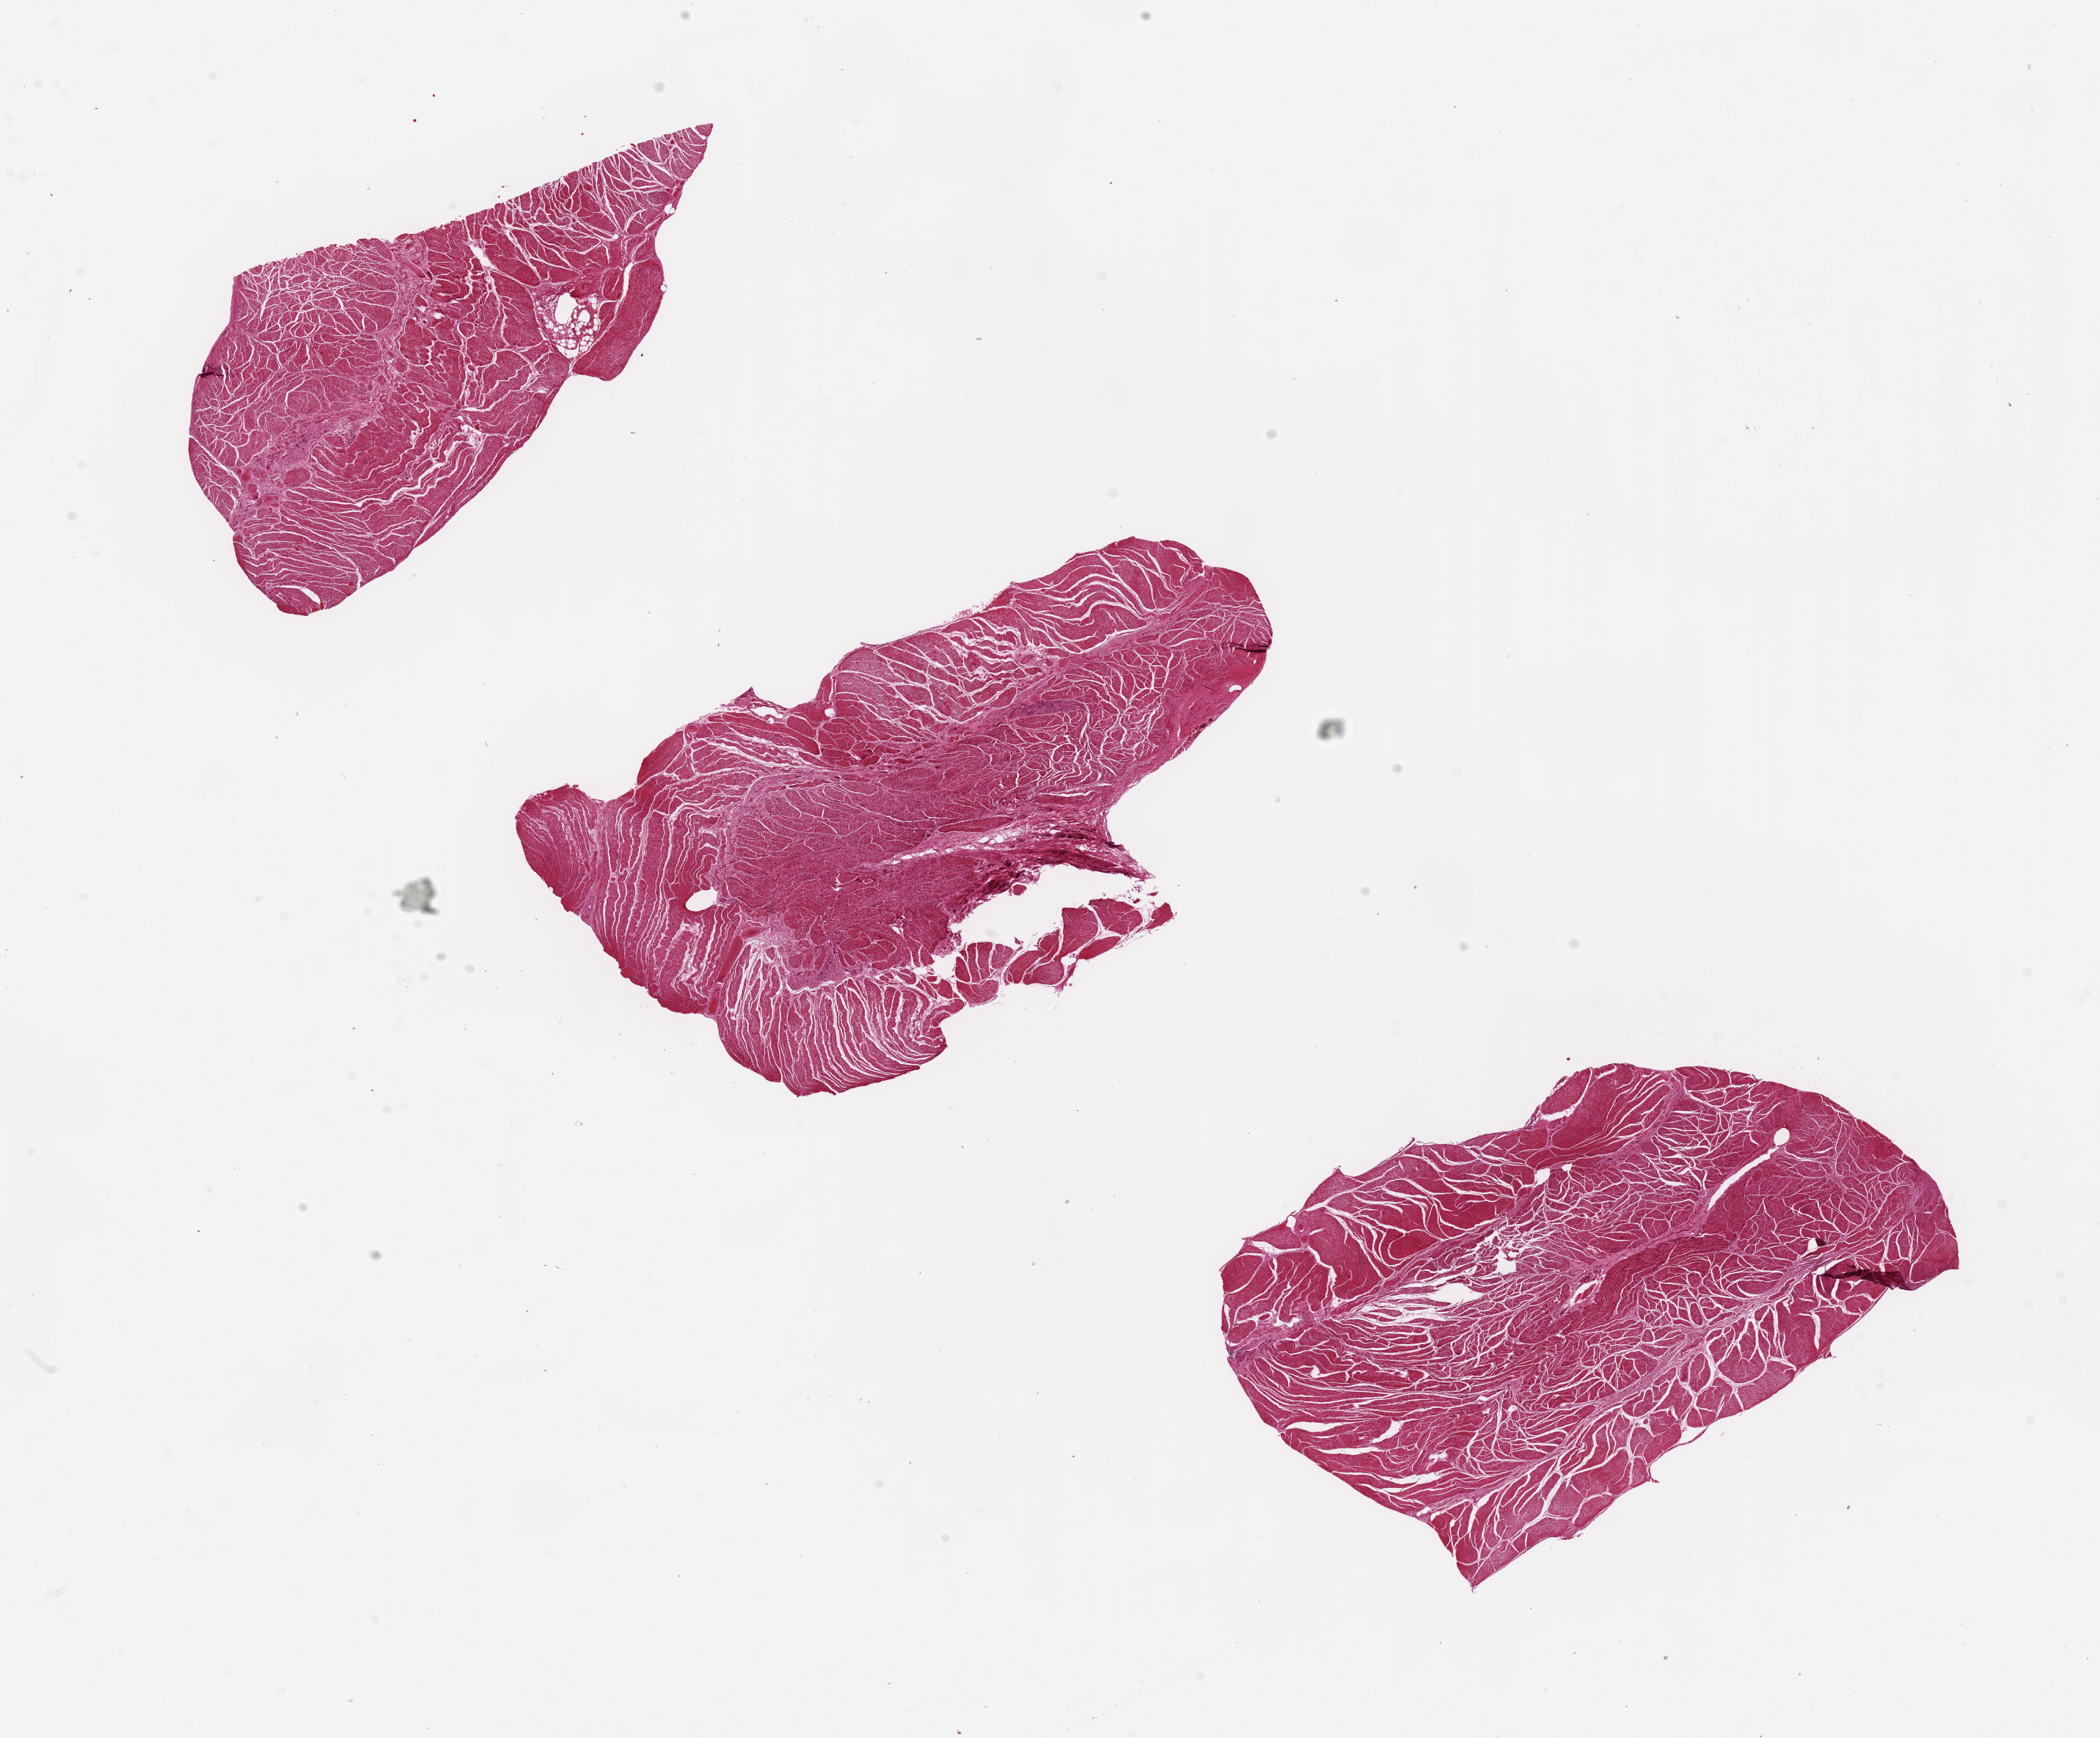
Whole-slide image, H&E stain, brightfield, a low-resolution overview of the entire scanned area, about 22.6 x 18.7 mm (from a 20x scan). PAXgene-fixed paraffin-embedded (PFPE) section. Section of esophageal muscle (target tissue). Tissue donor sample. Male donor.
* pathologist's review note for this sample: 3 pieces, up to 7x4 mm